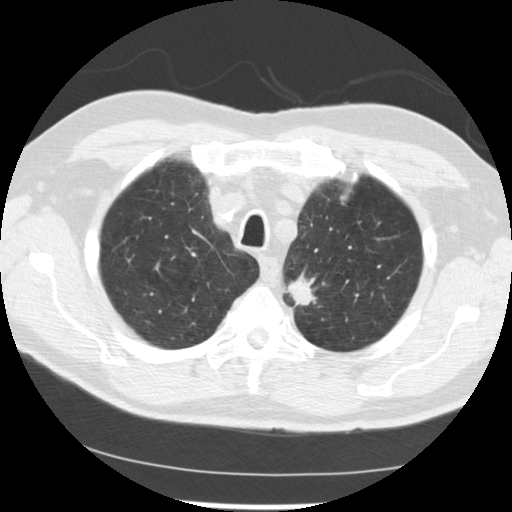
Low-dose screening chest CT, one axial slice. Slice 203 of 249 in the series (ordered by position). Reconstruction kernel STANDARD. Lung window (W 1500 / L -600 HU). 512 × 512 image matrix, field of view 341 × 341 mm.
Outlined on this slice (outlined manually by an expert reader):
- lesion 2 (tumor, upper lobe of left lung): bounding box [x1, y1, x2, y2] px = [288, 277, 316, 306]